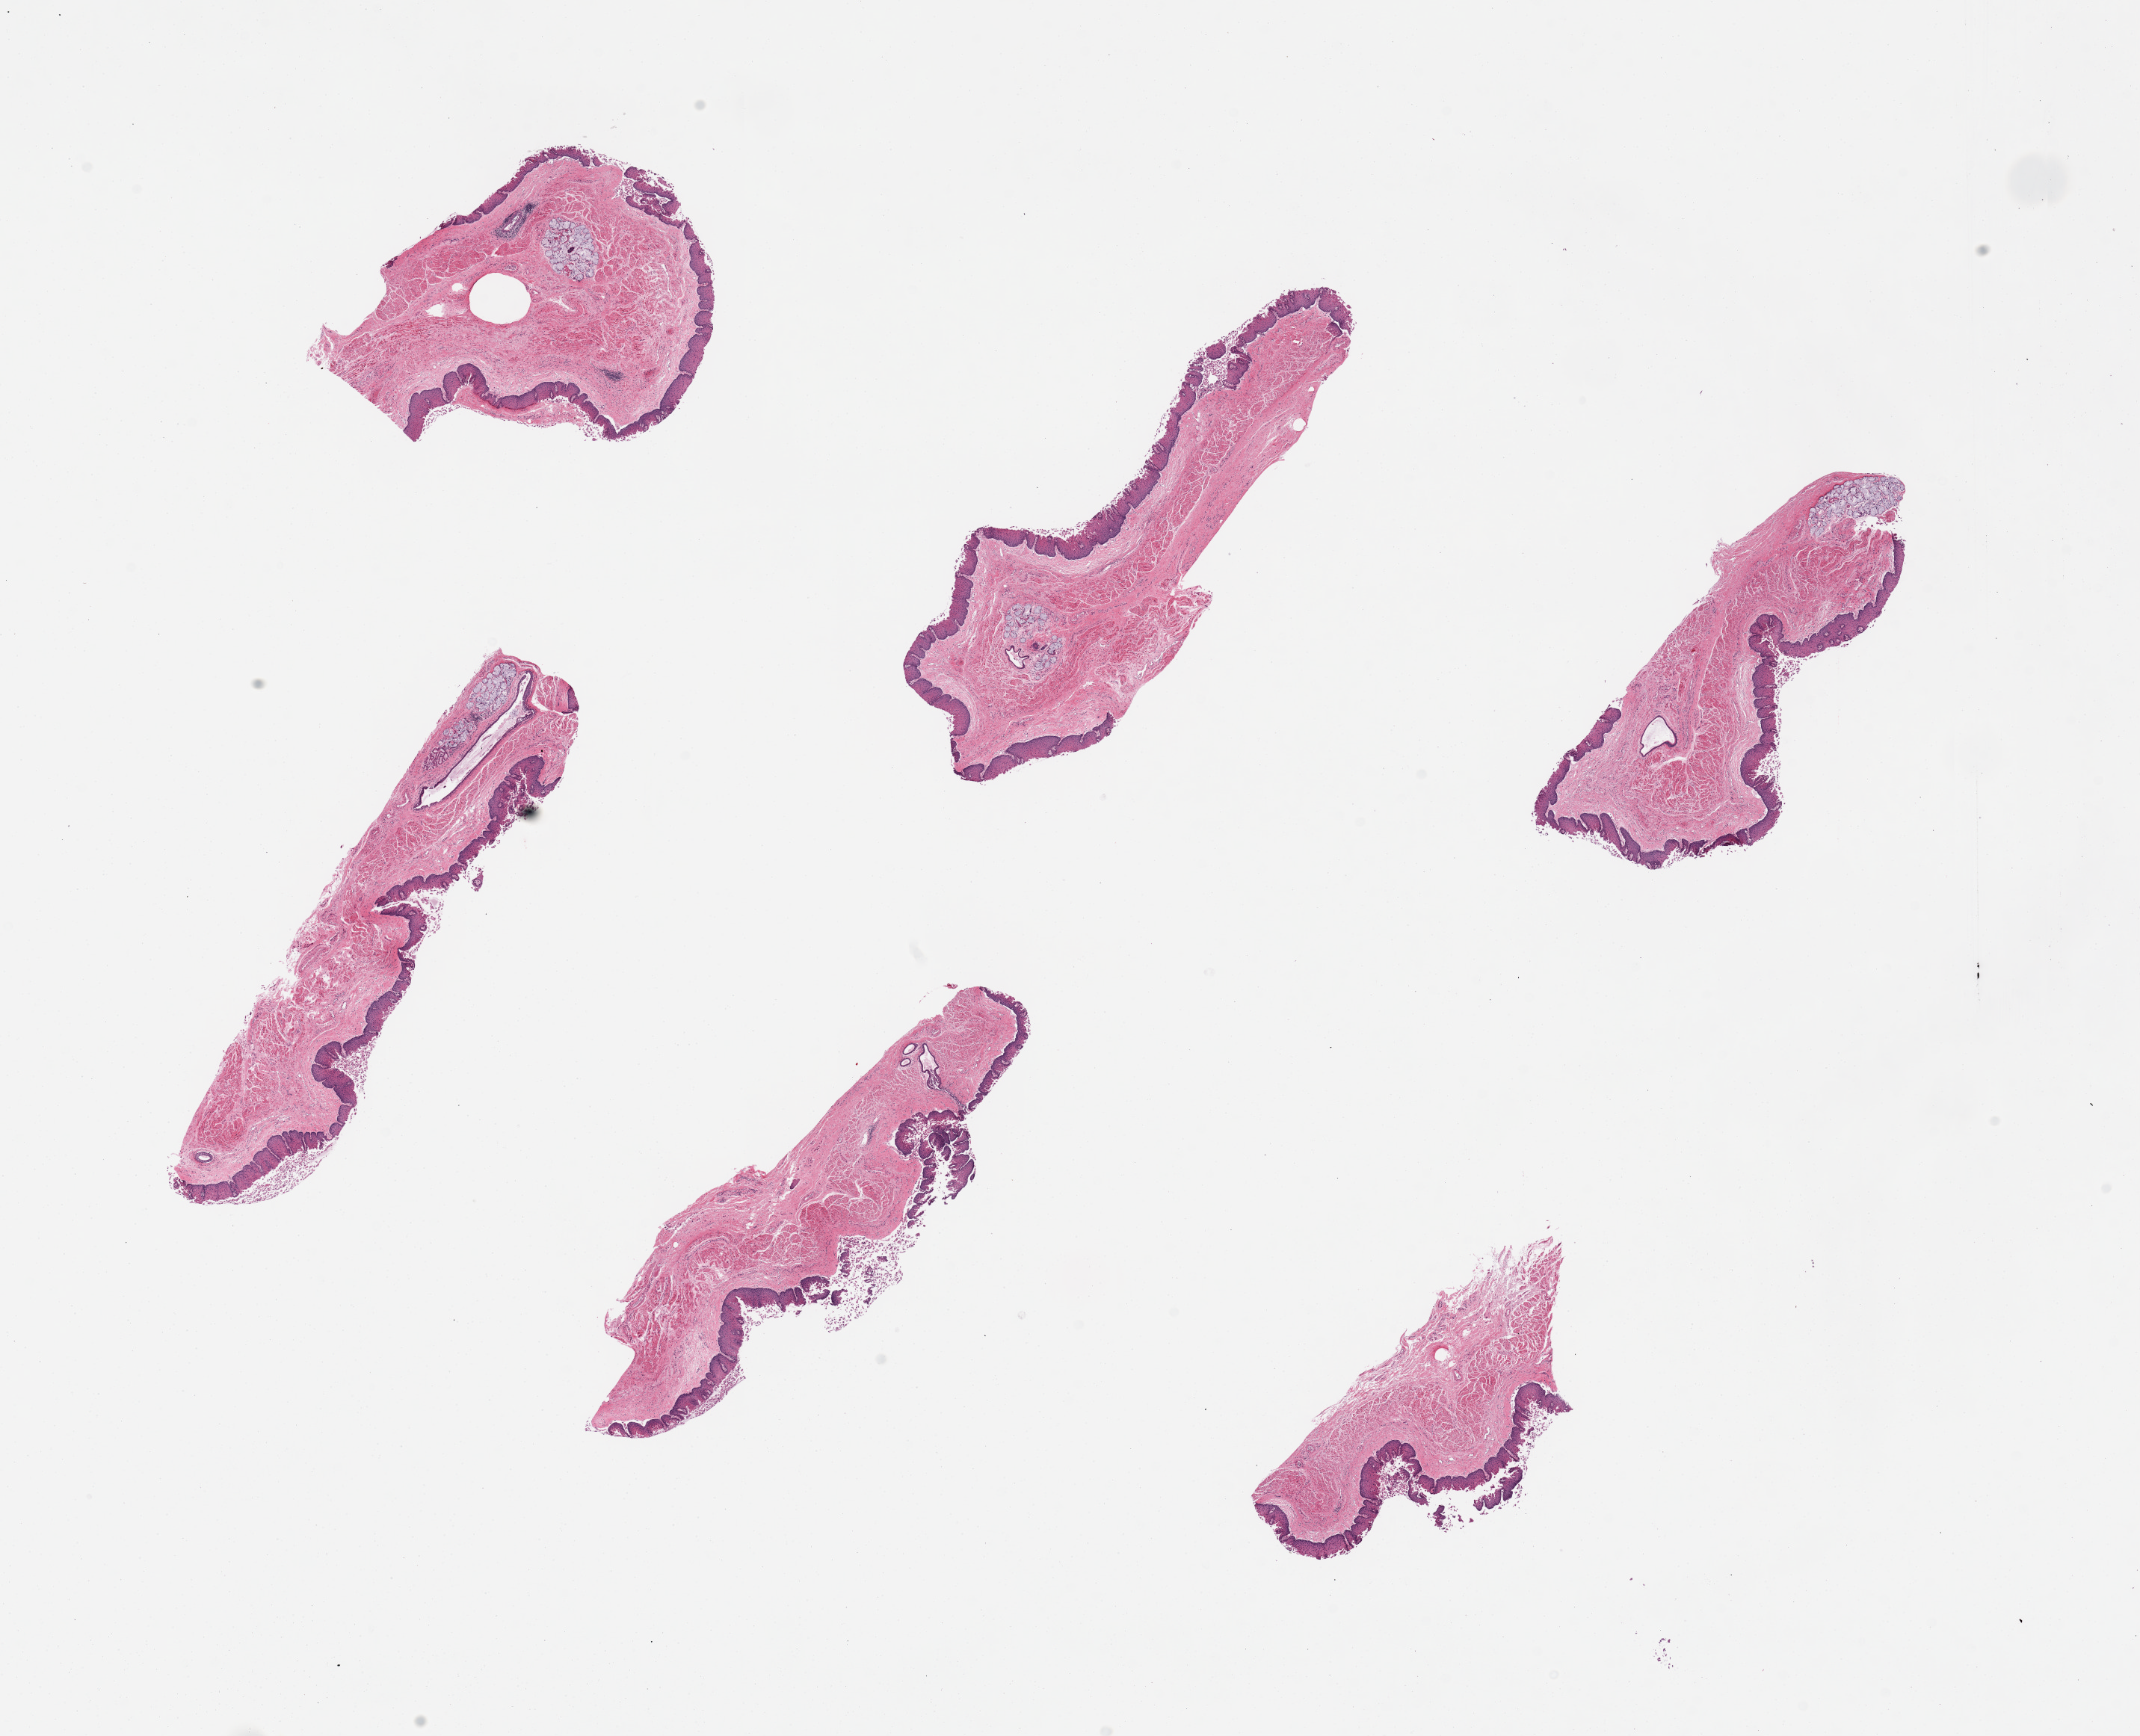
Digitized H&E-stained section, a low-resolution overview of the entire scanned area, about 22.6 x 18.4 mm, PAXgene-fixed, paraffin-embedded tissue, target tissue: esophageal mucous membrane, donor tissue sample. Donor: female.
- reviewer comment on this tissue sample: 6 pieces; partial epithelial sloughing; prominent glandular ducts [c/w/ reflux]